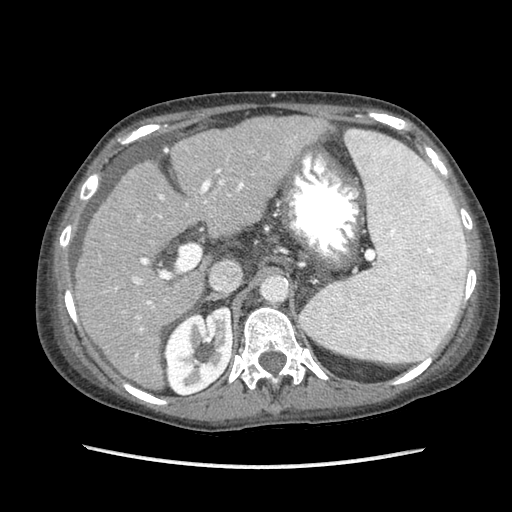
Contrast-enhanced abdominal CT (liver protocol), one axial slice. Slice 53 of 87 in the series (ordered by position). Reconstruction kernel STANDARD. 120 kVp. Soft-tissue window (W 400 / L 40 HU). 2.5 mm slice thickness. 512 × 512 image matrix. From the clinical record (not read from this slice): diagnosis: hepatocellular carcinoma (patient treated with transarterial chemoembolisation; whether this scan precedes or follows treatment is not stated here); TNM stage (as recorded): Stage-IIIB; Child-Pugh class: A; tumour differentiation: no biopsy.
Outlined on this slice (semi-automatic segmentation, software-assisted and operator-edited):
- liver parenchyma outside the tumour (the mass and vessels are separate outlines, so this box may not span the whole liver): bounding box <76,116,394,389> (left, top, right, bottom; pixels)
- liver vessels: <115,130,394,357>